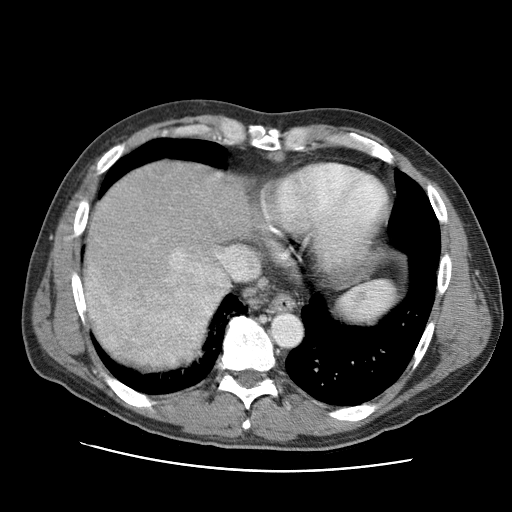
Contrast-enhanced abdominal CT (liver protocol), one axial slice. Position 82 of 95 along the scan axis. One of 2 acquisitions stored at this slice position. Soft-tissue window (W 400 / L 40 HU). 512 × 512 image matrix, field of view 360 × 360 mm. From the clinical record (not read from this slice): diagnosis: hepatocellular carcinoma (patient treated with transarterial chemoembolisation; whether this scan precedes or follows treatment is not stated here); TNM stage (as recorded): Stage-IVA; Child-Pugh class: A; tumour differentiation: moderately differentiated.
Annotated regions visible in this slice (semi-automatically segmented with operator editing):
- liver parenchyma outside the tumour (the mass and vessels are separate outlines, so this box may not span the whole liver): bounding box <84,162,260,356> (left, top, right, bottom; pixels)
- mass: <84,248,227,370>
- liver vessels: <217,174,257,276>